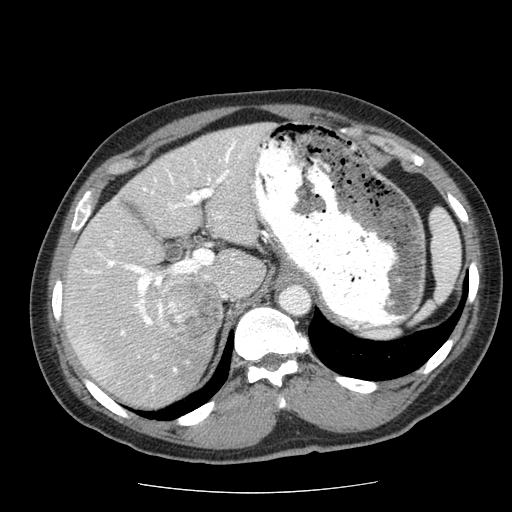
Contrast-enhanced abdominal CT (liver protocol), one axial slice; position 40 of 85 along the scan axis; 120 kVp; soft-tissue window (W 400 / L 40 HU); 2.5 mm slice thickness; 512 × 512 image matrix, field of view 360 × 360 mm. From the clinical record (not read from this slice): diagnosis: hepatocellular carcinoma (patient treated with transarterial chemoembolisation; whether this scan precedes or follows treatment is not stated here); TNM stage (as recorded): Stage-IIIA; Child-Pugh class: A; tumour differentiation: well differentiated; tumour nodularity: multinodular.
Outlined on this slice (semi-automatically segmented with operator editing):
- abdominal aorta: bounding box <279,284,310,315> (left, top, right, bottom; pixels)
- liver parenchyma outside the tumour (the mass and vessels are separate outlines, so this box may not span the whole liver): <64,122,272,408>
- mass: <164,279,221,339>
- liver vessels: <78,139,242,379>